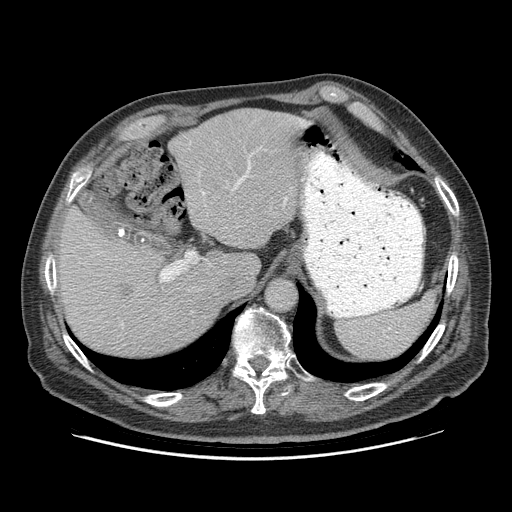
Contrast-enhanced abdominal CT (liver protocol), one axial slice. Slice 67 of 95 in the series (ordered by position). Soft-tissue window (W 400 / L 40 HU). 512 × 512 image matrix, field of view 400 × 400 mm. From the clinical record (not read from this slice): diagnosis: hepatocellular carcinoma (patient treated with transarterial chemoembolisation; whether this scan precedes or follows treatment is not stated here); TNM stage (as recorded): Stage-IVB; Child-Pugh class: A; tumour nodularity: uninodular.
Annotated regions visible in this slice (semi-automatically segmented with operator editing):
- abdominal aorta: bounding box <267,279,296,310> (left, top, right, bottom; pixels)
- liver parenchyma outside the tumour (the mass and vessels are separate outlines, so this box may not span the whole liver): <56,108,306,356>
- mass: <117,282,133,297>
- liver vessels: <161,121,303,282>